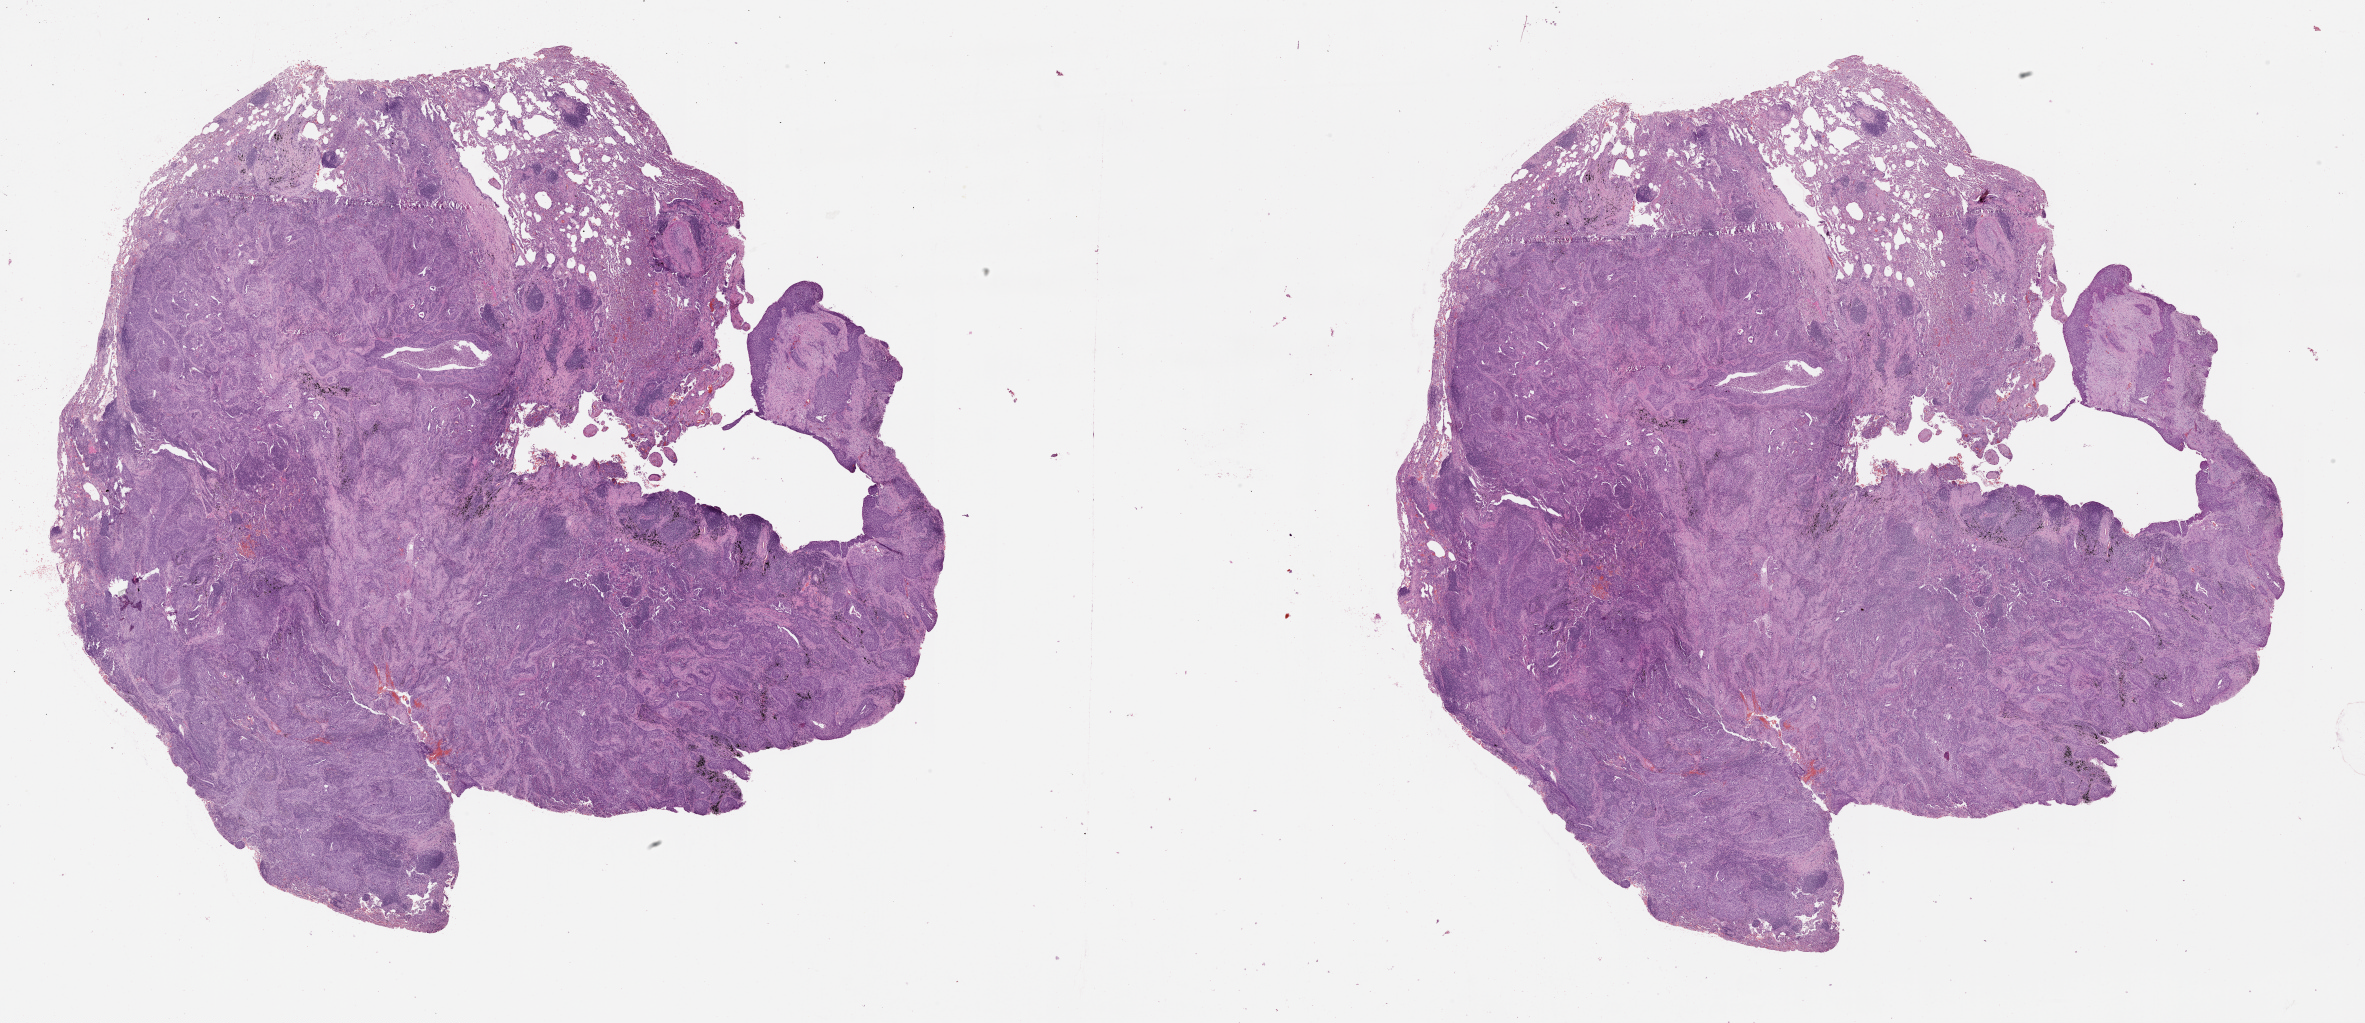
Digitized H&E tissue section (whole slide), low-resolution overview of the scanned area, about 38.1 x 16.5 mm (acquisition: 20x scan); tumour tissue sample, lung. Male, 74 y/o.
• patient diagnosis (cohort enrolment): squamous cell carcinoma (lung)